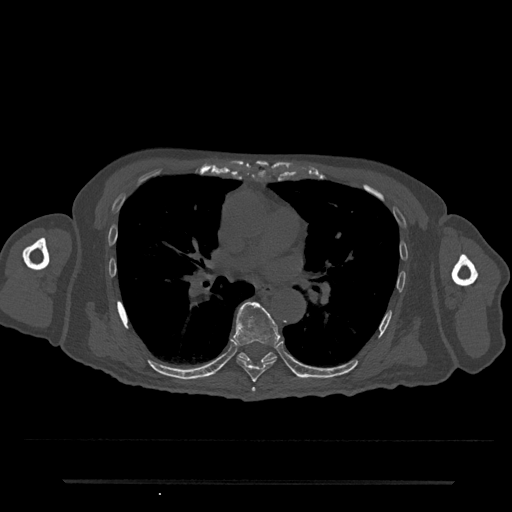
CT including the spine, one axial slice; slice 461 of 797 in the series (ordered by position); 120 kVp; bone window (W 1800 / L 400 HU); 0.5 mm slice thickness; 512 × 512 image matrix. Male patient, age 74 years. From the clinical record (not read from this slice): primary cancer: prostate.
Outlined on this slice (semi-automatic segmentation, software-assisted and operator-edited):
- T6 vertebra: box from (x=251, y=387) to (x=256, y=392) px
- T7 vertebra: (x=233, y=301)–(x=281, y=383)
- T8 vertebra: (x=238, y=352)–(x=276, y=364)